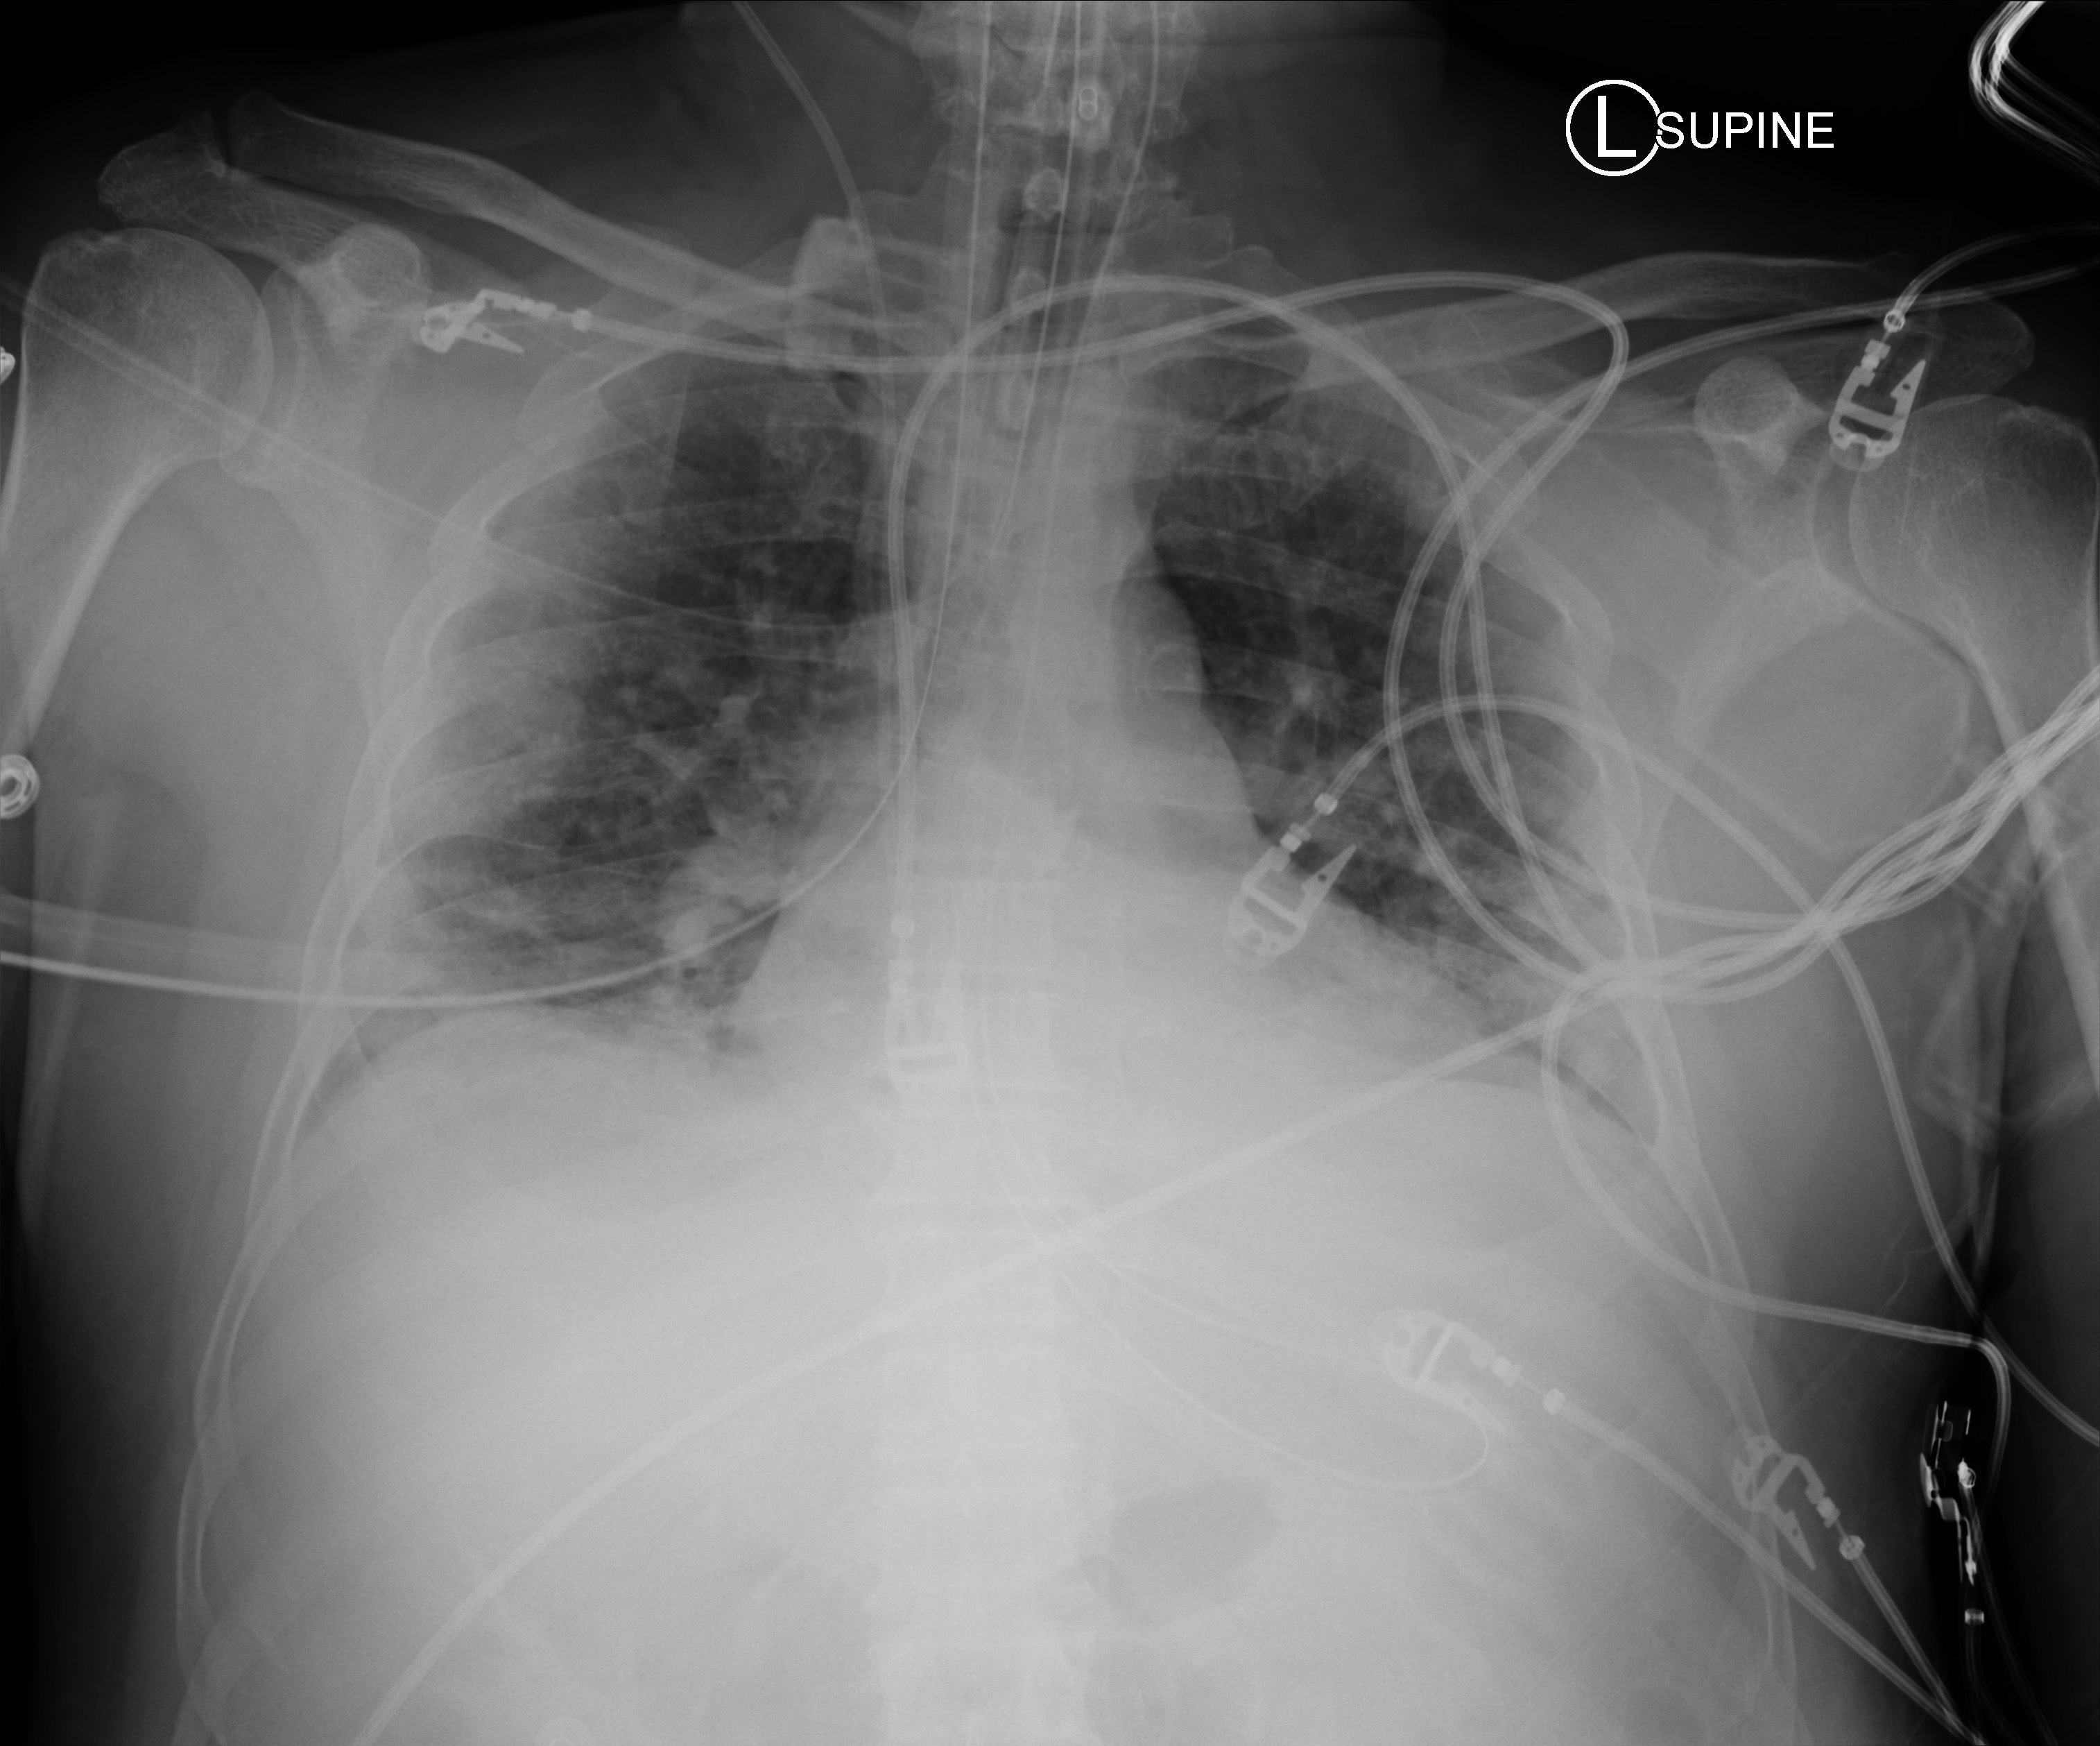
Portable chest radiograph. Male patient hospitalised with COVID-19, age 18–59 years.
Admission-level facts for this patient (not findings on this image; timing relative to this image not recorded):
- chronic kidney disease (admission record): no
- mechanically ventilated during this hospital stay: yes